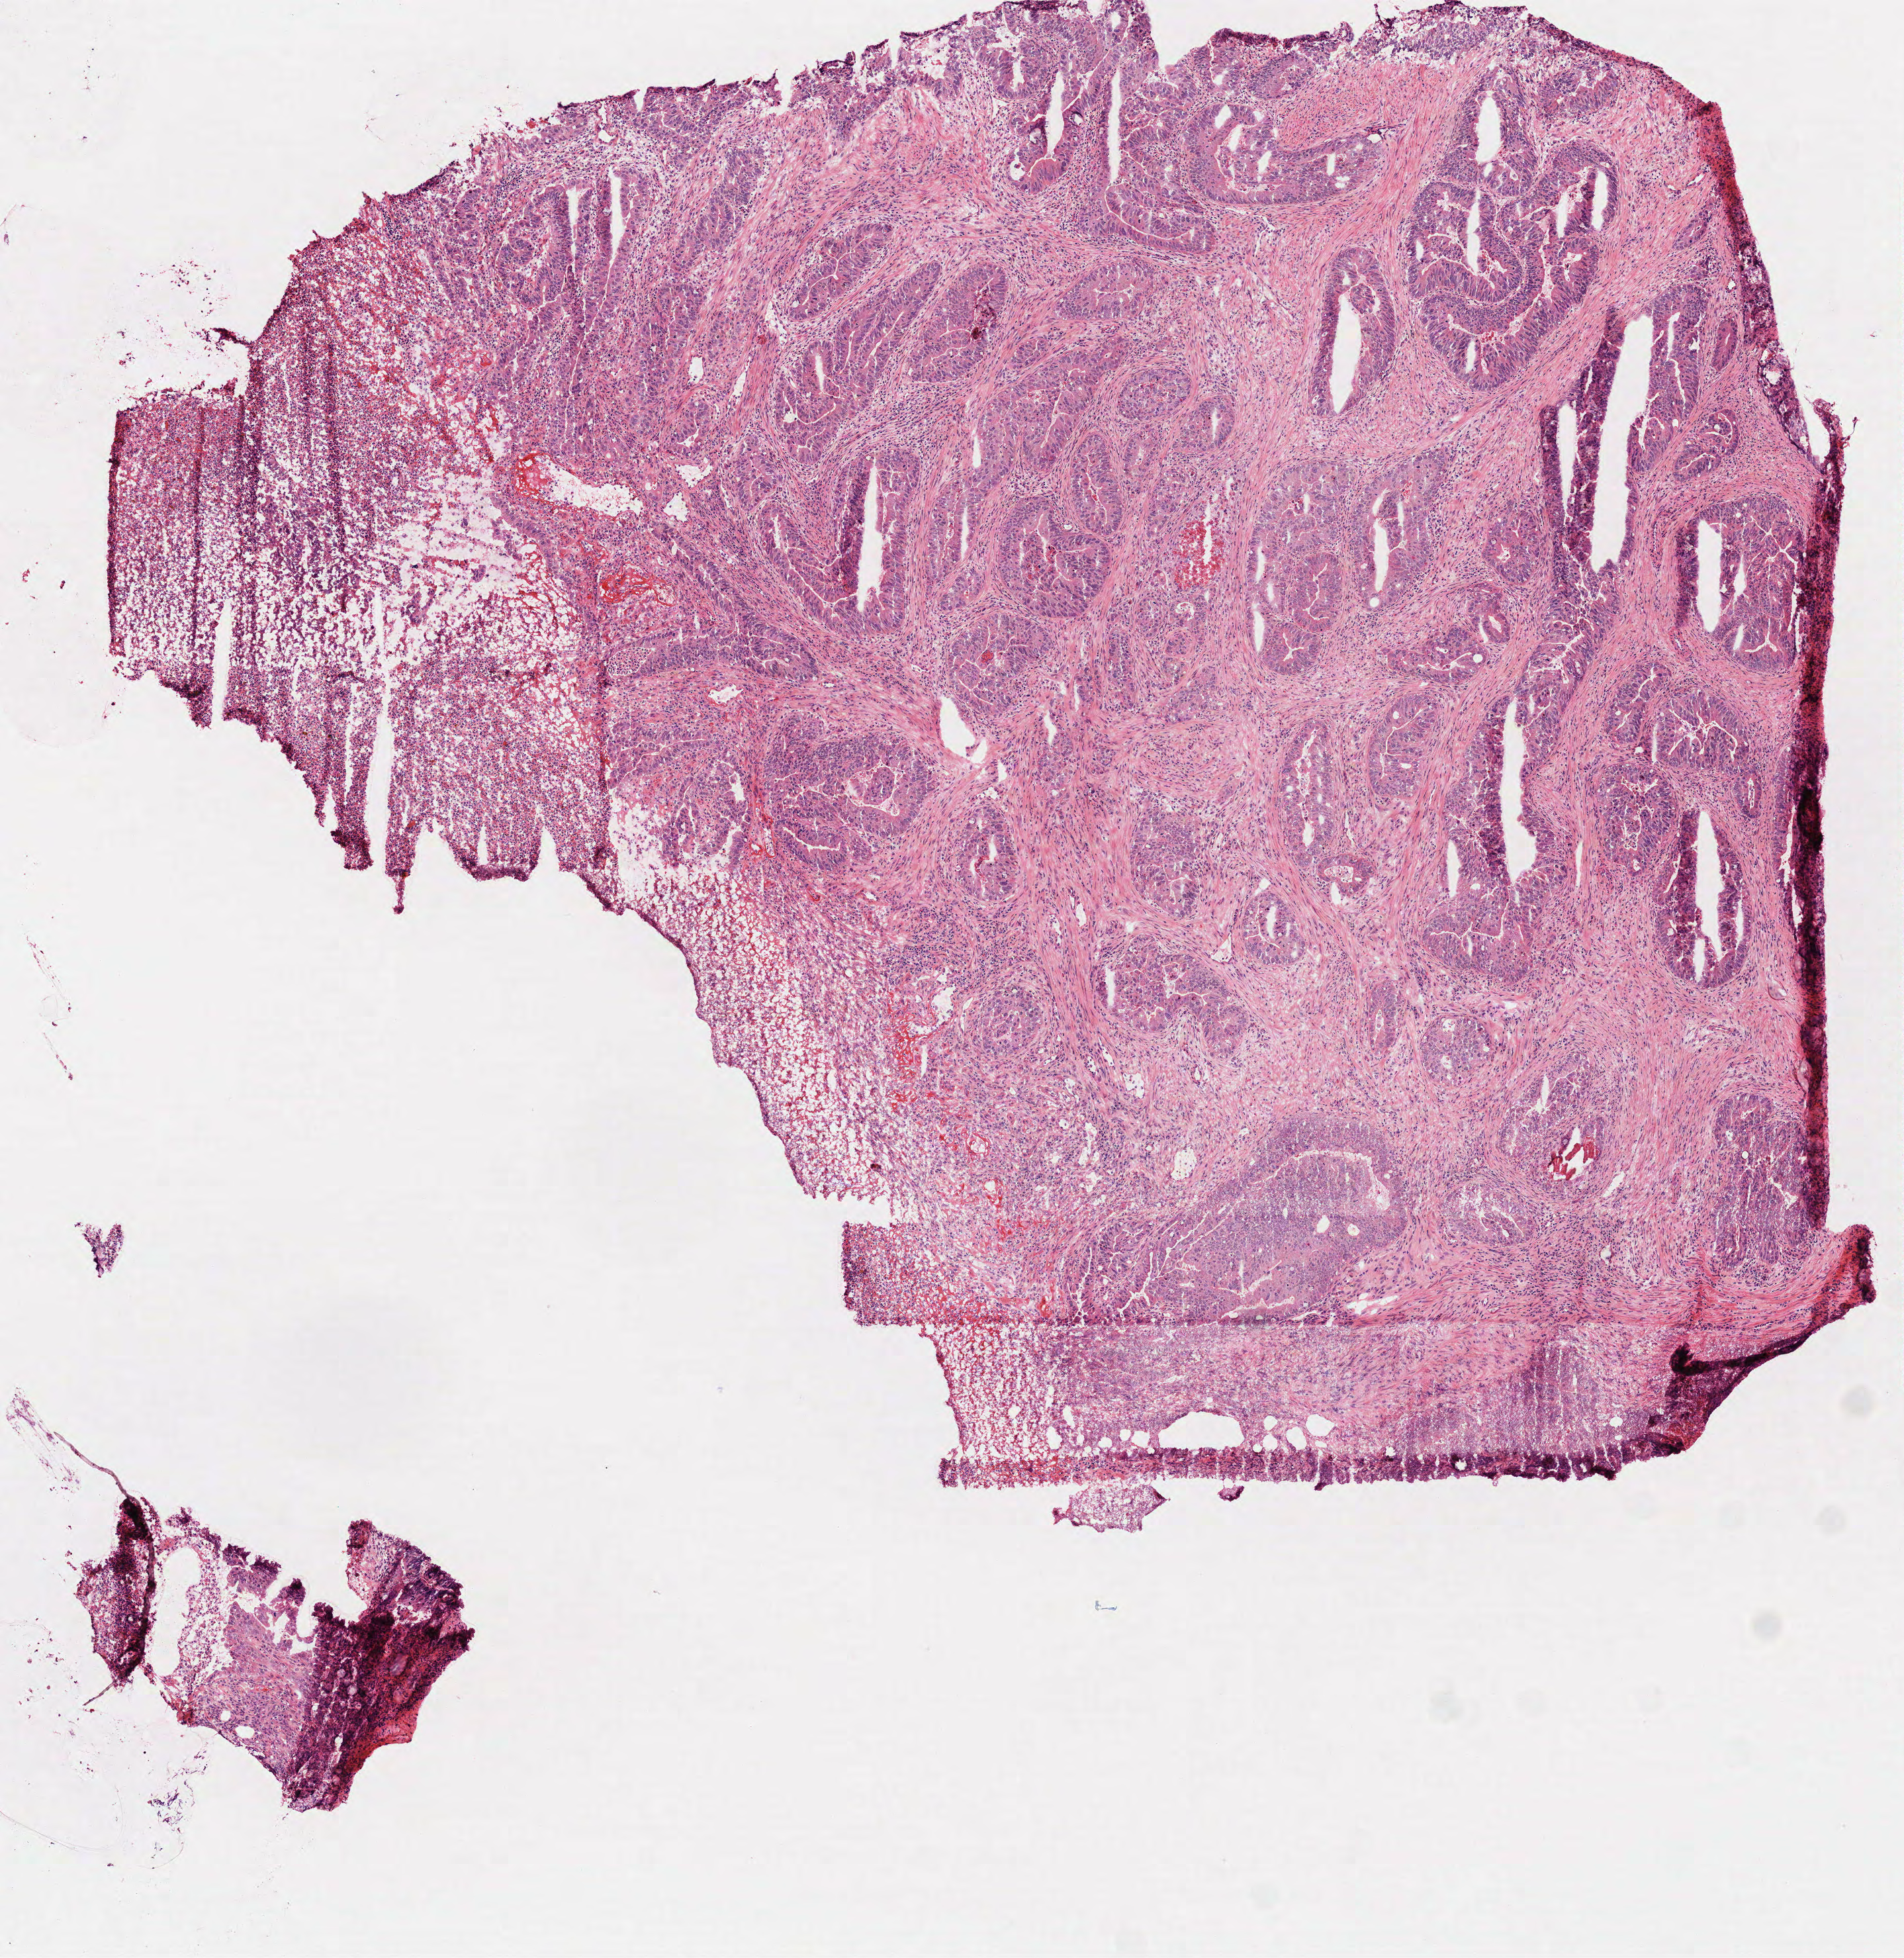
Hematoxylin and eosin (H&E) stained whole-slide image — a low-resolution overview of the entire scanned area, about 5.8 x 6.0 mm (acquisition: 40x scan). Frozen section from the top of the tissue portion. Colon, primary tumour sample. Patient: female, age at initial diagnosis 51 years. Slide review estimates, as recorded: tumour cells 65%, tumour nuclei 65%, normal cells 0%, stromal cells 30%, necrosis 5%.
TNM: T2 N0 M0. AJCC pathologic stage: I (7th edition). Diagnosis: Adenocarcinoma, NOS.